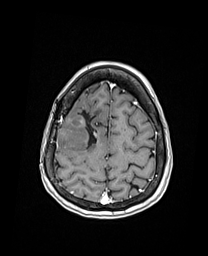
Brain MRI from a brain-tumour surgery series, one axial slice; position 44 of 192 along the scan axis; T1-weighted post-contrast; 1 mm slice thickness; 208 × 256 image matrix, field of view 208 × 256 mm. Case-level facts recorded for this patient, not image findings: histopathology: Oligodendroglioma; WHO grade: 3; IDH mutation: yes; tumour location: Right Frontal.
Structures marked on this image (outlined manually by an expert reader):
- previous resection cavity: bounding box [x1, y1, x2, y2] px = [72, 109, 88, 148]